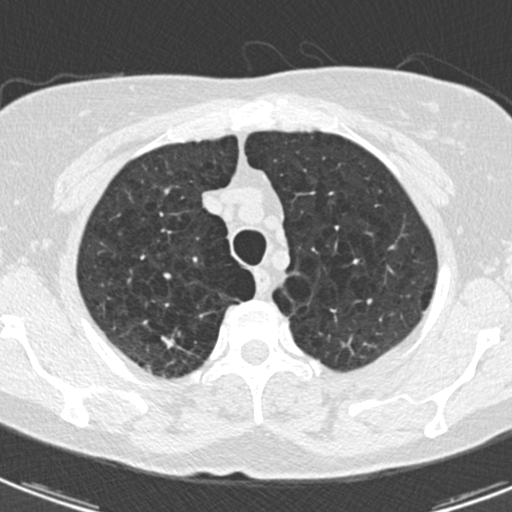
Axial slice from a low-dose chest CT screening exam; third screening round (two years after baseline); lung window (W 1500 / L -600 HU); 2 mm slice thickness; standard (soft-tissue) reconstruction kernel (B30f); slice 28 of 174 in the series. Female participant, aged 59 years at enrolment. Current smoker at enrolment.
- Lesion marked by an expert reader, bounding box [x1, y1, x2, y2] px = [134, 321, 196, 368].
- Screening reader's record for this exam (one nodule recorded; not confirmed to be the boxed lesion): non-calcified nodule or mass ≥4 mm, right upper lobe, 12 × 7 mm, spiculated (stellate) margins, soft tissue attenuation, pre-existing on the prior screen: yes; interval growth: yes.
- Official screen result: positive, other.
- Later outcome: lung cancer diagnosed 32 days after this screen — adenocarcinoma, NOS, right upper lobe, poorly differentiated (G3), stage IA (AJCC 6th edition), 20 mm at pathology.